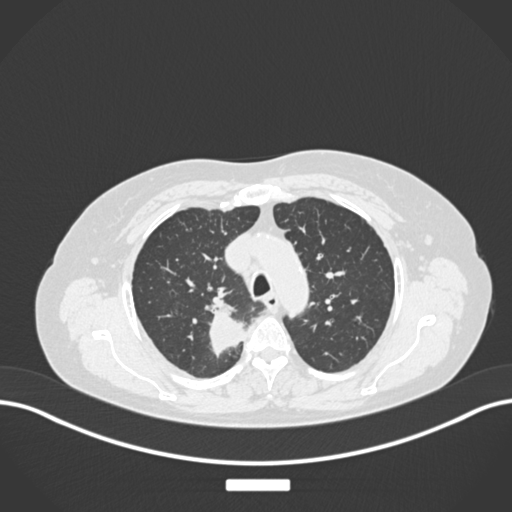
Chest CT, one axial slice. Position 192 of 237 along the scan axis. Reconstruction kernel B30f. 120 kVp. Lung window (W 1500 / L -600 HU). 512 × 512 image matrix, field of view 400 × 400 mm. Female patient, age 62 years. From the clinical record (not read from this slice): clinical TNM (as recorded): T1c N1 M0.
Outlined on this slice (rectangle marked by the reading radiologist):
- lung tumour (recorded histology: squamous cell carcinoma): bounding box [x1, y1, x2, y2] px = [207, 304, 251, 360]